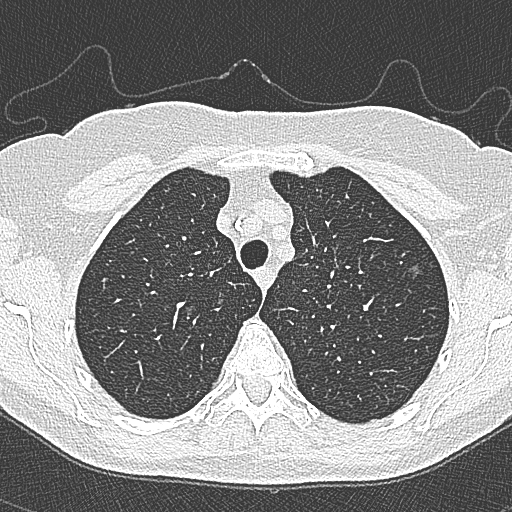
Chest CT (low-dose screening protocol), one axial image. Second annual screen. Lung window (W 1500 / L -600 HU). 512 × 512 image matrix, field of view 298 × 298 mm. Female, age 65 years at enrolment. Current smoker at enrolment.
• Expert reader's lesion annotation, bounding box (x1, y1, x2, y2) in pixels: (396, 251, 433, 283).
• The screening reader recorded 4 non-calcified nodules or masses ≥4 mm on this exam (left upper lobe, left upper lobe, left upper lobe, right lower lobe); which of them this box marks is not recorded.
• Official screen result: positive, change unspecified: nodule(s) >= 4 mm or enlarging nodule(s), mass(es), or other non-specific abnormalities suspicious for lung cancer.
• Participant outcome: lung cancer diagnosed 54 days after this screen — bronchiolo-alveolar carcinoma, non-mucinous, left upper lobe, stage IA (AJCC 6th edition), 10 mm at pathology.